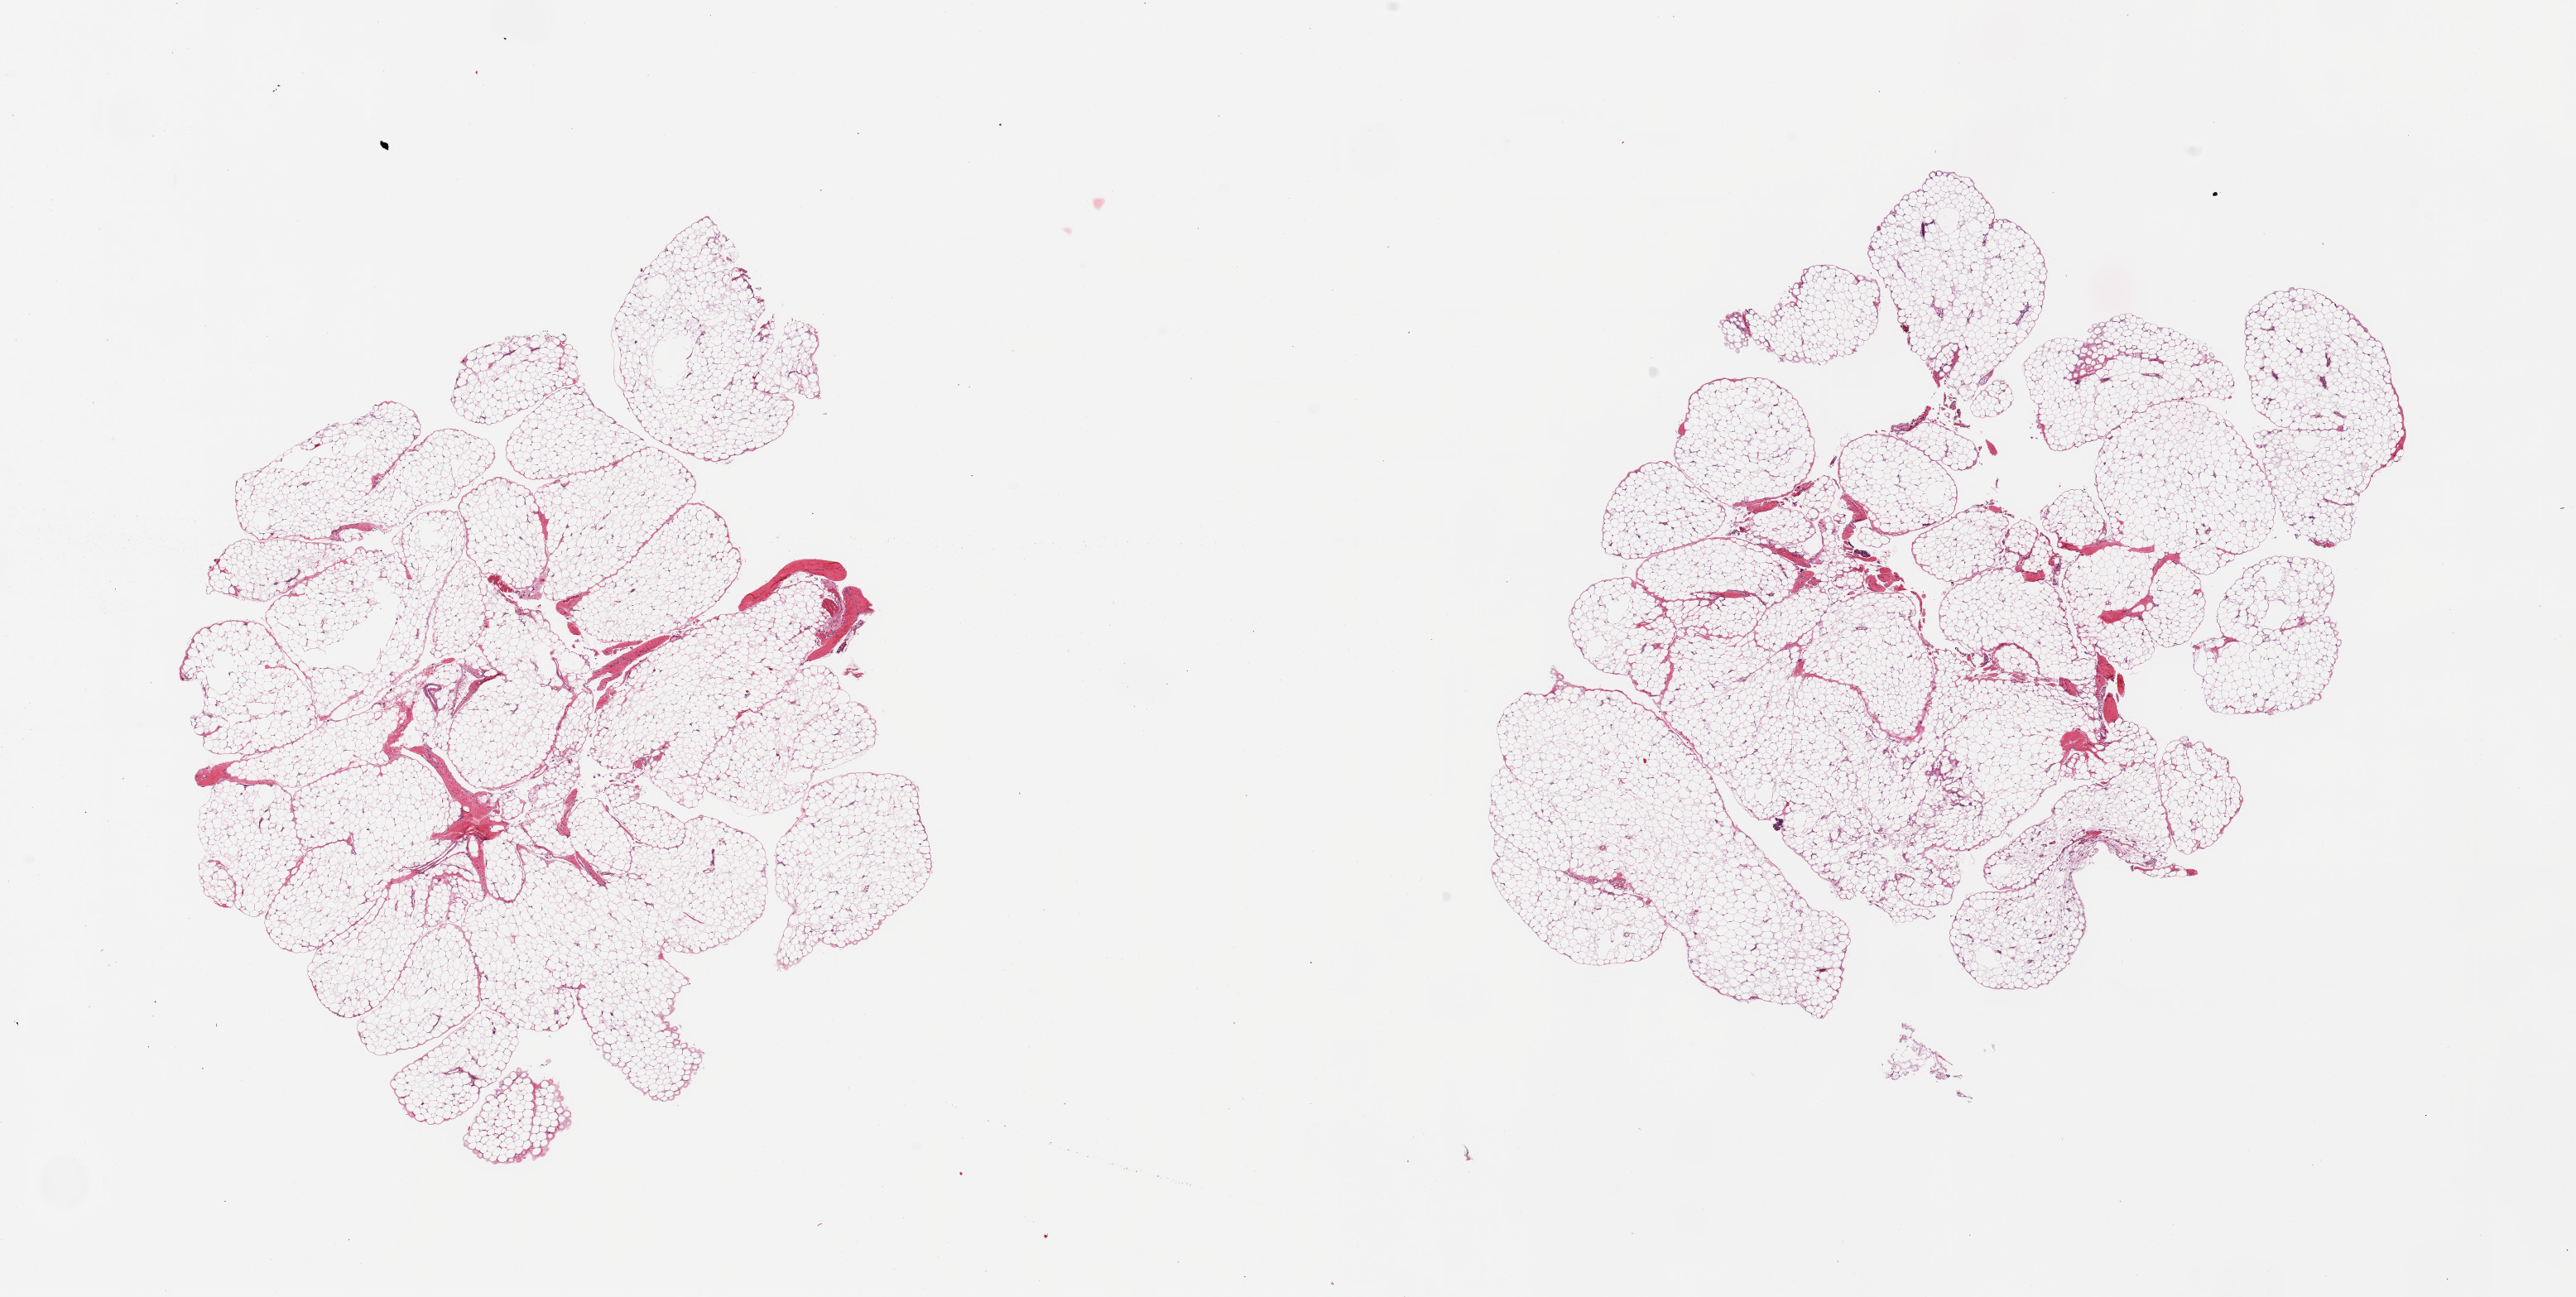
H&E whole-slide image — a low-resolution overview of the entire scanned area, about 24.6 x 12.4 mm (slide scanned at 20x); PAXgene-fixed, paraffin-embedded tissue; sampled site (target tissue): omentum; tissue donor sample. Donor: male.
Review note (as recorded): 2 pieces; lobulated mature adipose tissue with scant fibrovascular component, nerves and muscle fibers.